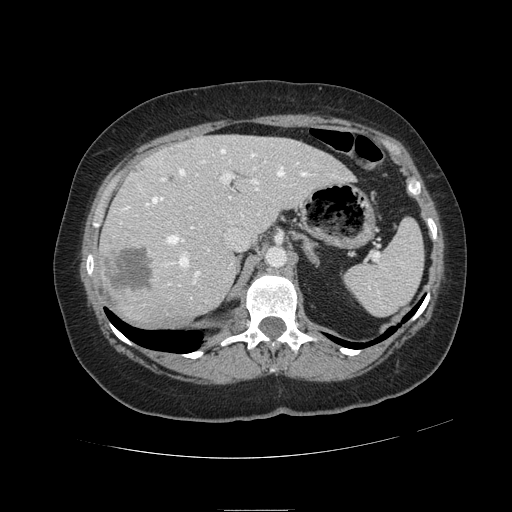
Contrast-enhanced abdominal CT, one axial slice; slice 75 of 121 in the series (ordered by position); soft-tissue window (W 400 / L 40 HU); 2.5 mm slice thickness; 512 × 512 image matrix. Female patient, age 52 years. From the clinical record (not read from this slice): diagnosis: colorectal cancer liver metastases, imaged before liver resection; multiple liver metastases: yes; largest metastasis: 6.3 cm; disease in both lobes: no.
Annotated regions visible in this slice (manually delineated by an expert):
- hepatic veins: box from (x=123, y=150) to (x=307, y=299) px
- liver: (x=100, y=136)–(x=352, y=324)
- planned liver remnant (the part of the liver to remain after resection): (x=167, y=136)–(x=352, y=233)
- portal vein (with intrahepatic branches): (x=120, y=161)–(x=258, y=284)
- liver metastasis: (x=106, y=246)–(x=154, y=292)